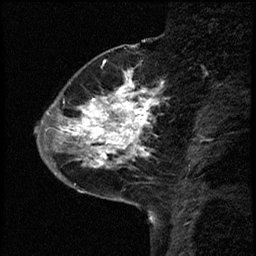
Breast MRI (dynamic contrast-enhanced), one sagittal slice. Position 17 of 68 along the scan axis. Dynamic contrast-enhanced study with each time point stored as its own series, time point 2 of 3 at this slice position (early post-contrast, ordered by acquisition time). 1.5 T. TE 4.2 ms, TR 17.6 ms. 2 mm slice thickness. 256 × 256 image matrix. Patient: female, 52 years. Case-level facts recorded for this patient, not image findings: setting: breast cancer imaged before/during neoadjuvant chemotherapy; receptor status: HER2-positive.
Annotated regions visible in this slice (semi-automatic segmentation, software-assisted and operator-edited):
- analysis volume of interest (the breast-tissue region the enhancement analysis was run in; not a lesion): bounding box (x1, y1, x2, y2) in pixels: (50, 61, 164, 184)
- tumour enhancement mask (voxels above the 100 % enhancement threshold inside the analysis volume of interest): (53, 73, 160, 174)